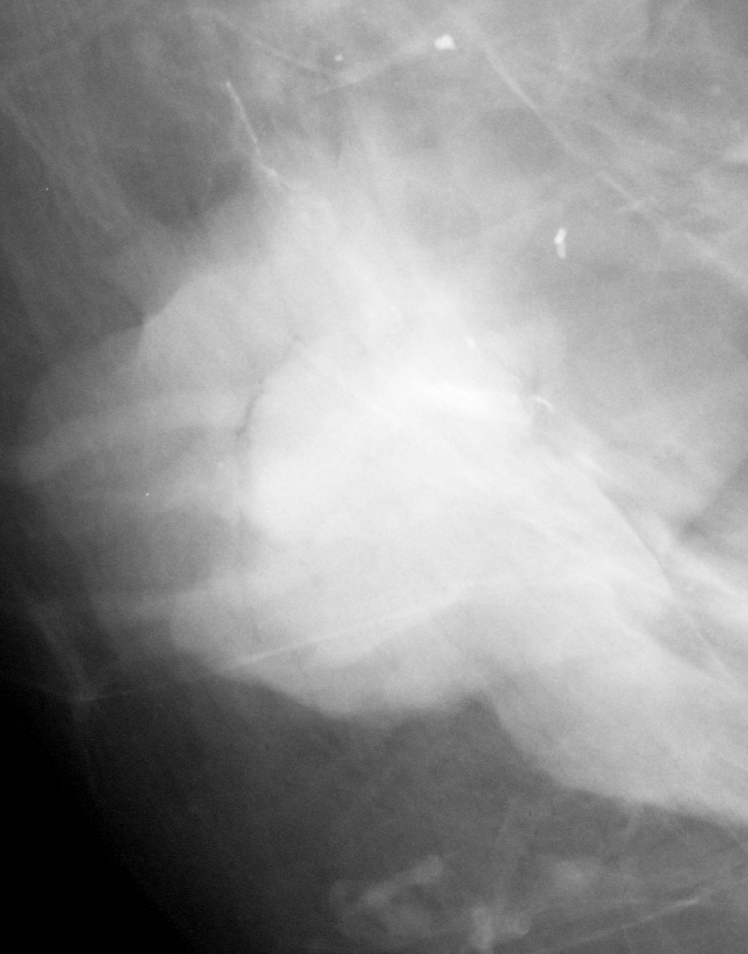
Cropped region of a digitized screen-film mammogram centred on a radiologist-marked abnormality, right breast, MLO view, BI-RADS breast density category 1 (scale 1–4).
- Marked abnormality: mass, shape lobulated, margins circumscribed; BI-RADS assessment category 5; pathology (as recorded): malignant.